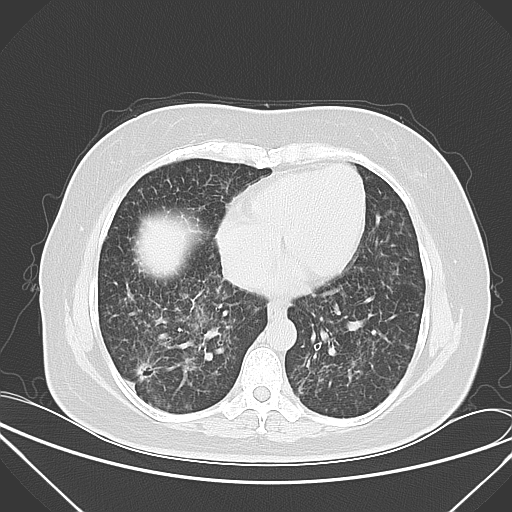
Chest CT, one axial slice; position 18 of 52 along the scan axis; lung window (W 1500 / L -600 HU); 5 mm slice thickness; 512 × 512 image matrix, field of view 386 × 386 mm. Patient: female, 50 years. From the clinical record (not read from this slice): clinical TNM (as recorded): T1c N0 M1a.
Annotated regions visible in this slice (rectangle marked by the reading radiologist):
- lung tumour (recorded histology: adenocarcinoma): bounding box [x1, y1, x2, y2] px = [132, 358, 162, 388]